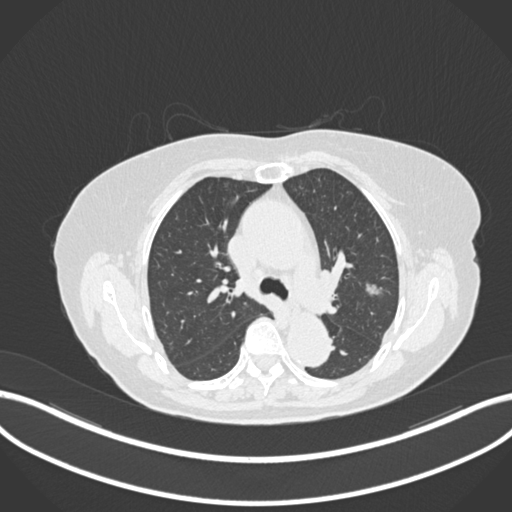
Chest CT, one axial slice; slice 108 of 168 in the series (ordered by position); 120 kVp; lung window (W 1500 / L -600 HU); 1 mm slice thickness; 512 × 512 image matrix, field of view 400 × 400 mm. Female patient, age 75 years. From the clinical record (not read from this slice): clinical TNM (as recorded): T1c N0 M0.
Structures marked on this image (bounding box drawn by a radiologist):
- lung tumour (recorded histology: adenocarcinoma): bounding box (x1, y1, x2, y2) in pixels: (361, 278, 384, 297)